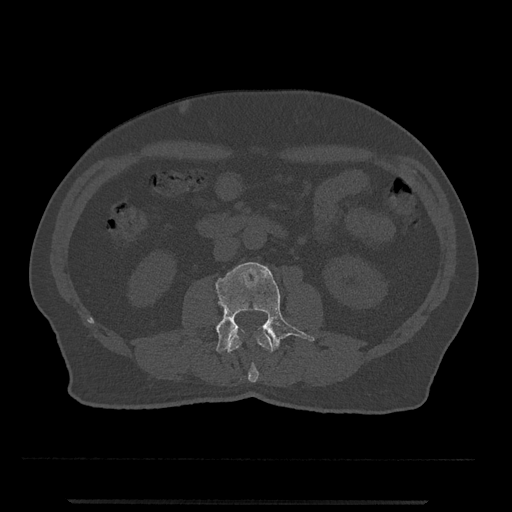
CT including the spine, one axial slice. Slice 219 of 797 in the series (ordered by position). Reconstruction kernel Br40s/3. Bone window (W 1800 / L 400 HU). 512 × 512 image matrix, field of view 419 × 419 mm. Male patient, age 63 years. Case-level facts recorded for this patient, not image findings: primary cancer: prostate.
Outlined on this slice (semi-automatic segmentation, software-assisted and operator-edited):
- L2 vertebra: box from (x=227, y=332) to (x=273, y=382) px
- L3 vertebra: (x=214, y=262)–(x=315, y=353)